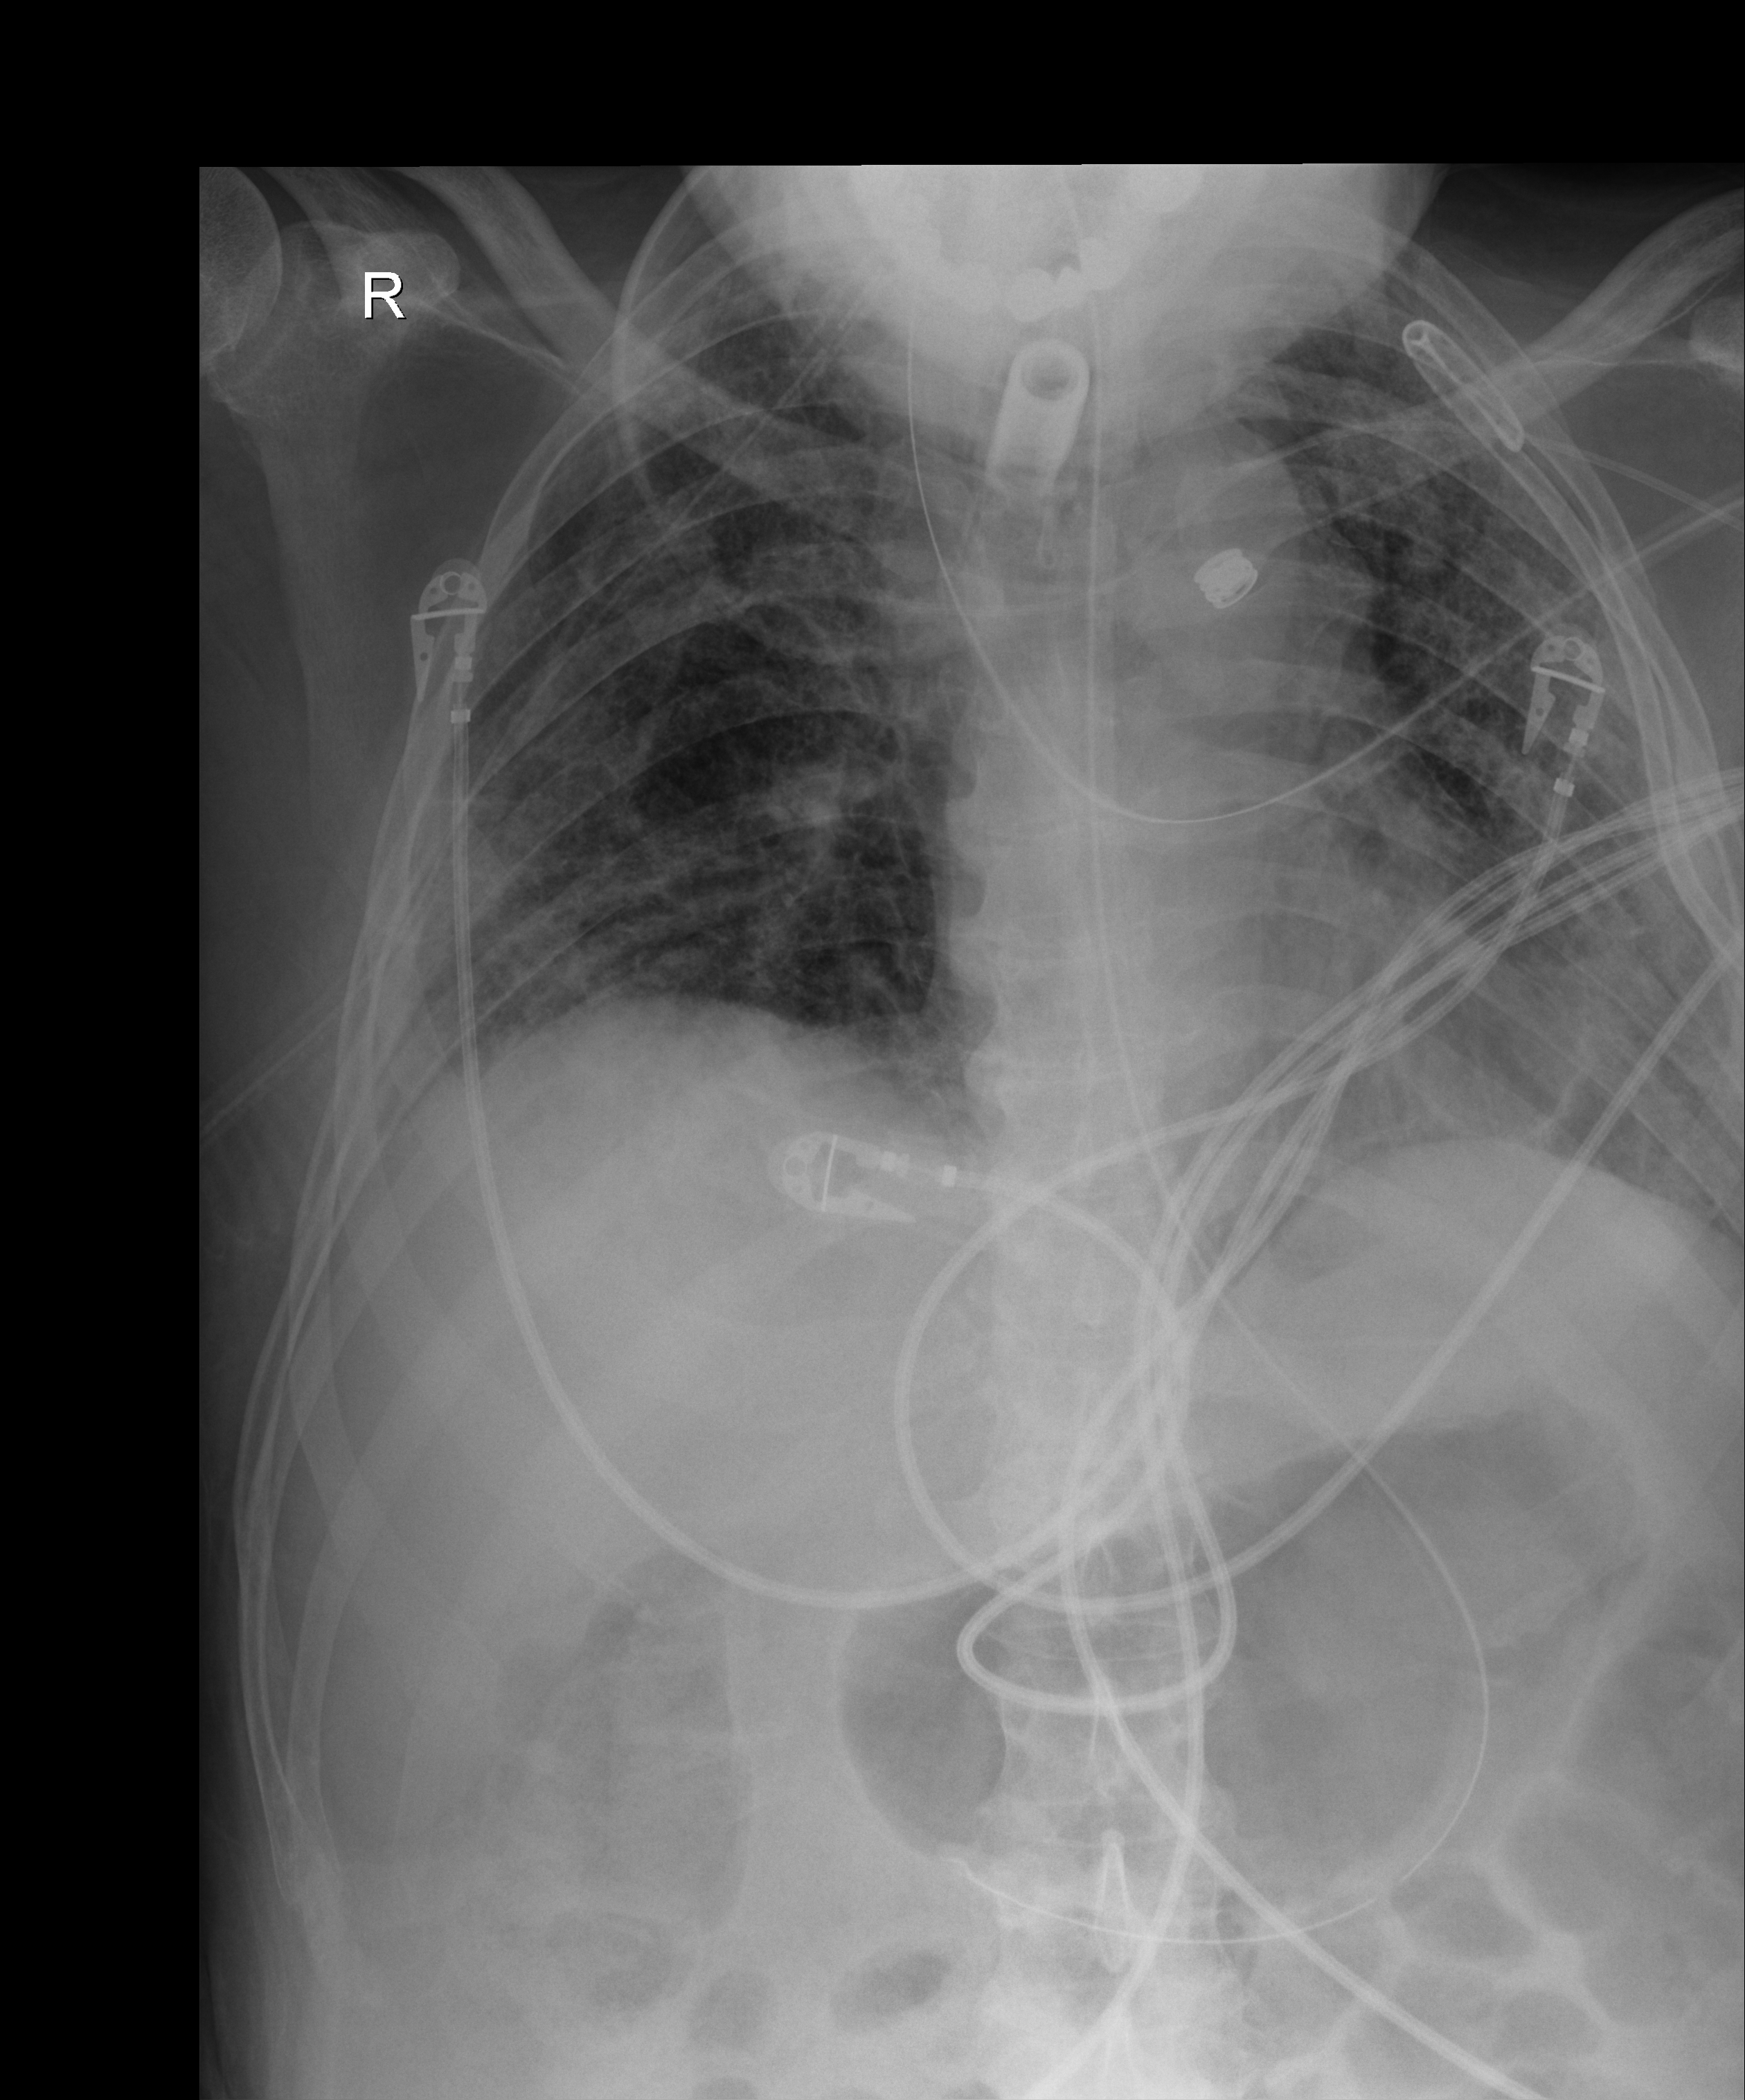
Chest X-ray (portable); anteroposterior (AP) projection. Patient hospitalised with COVID-19; male, aged 18–59 years.
Hospital-stay facts (about this admission, not read from this image; timing relative to this image not recorded): diabetes (admission record): no; mechanically ventilated during this hospital stay: yes.